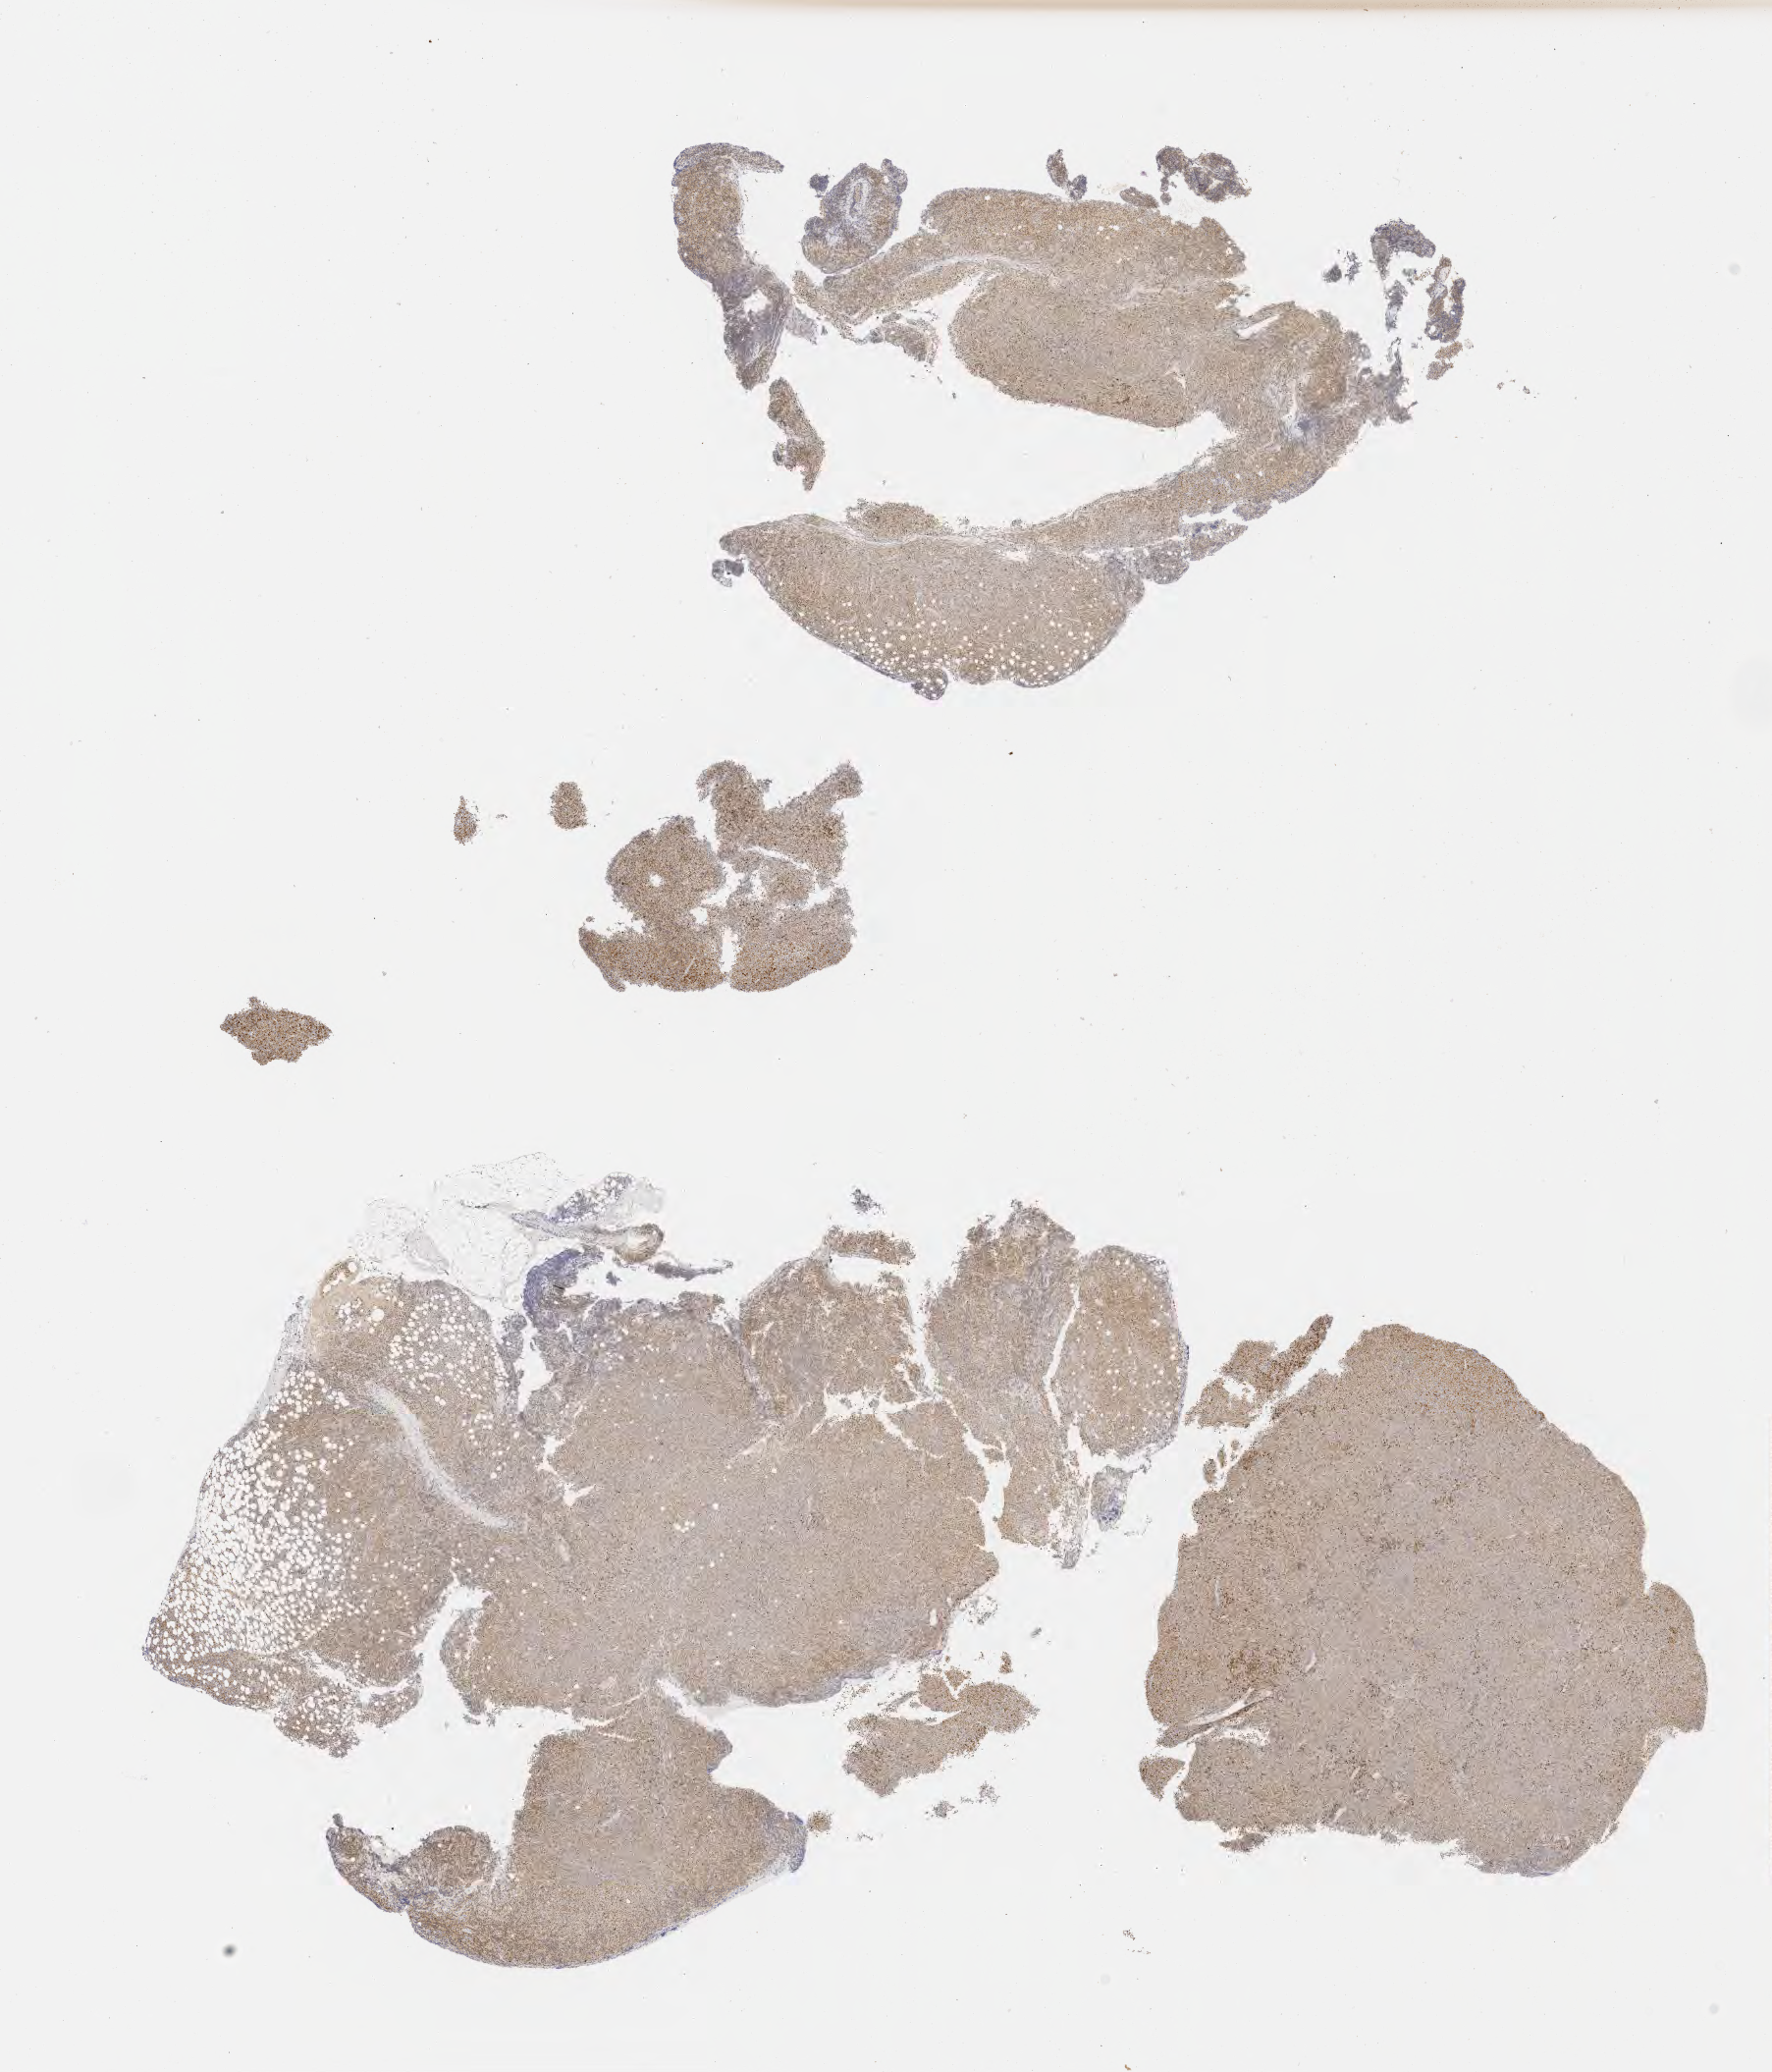
IHC for BCL6, whole-slide image — low-resolution overview of the scanned area, about 14.6 x 17.1 mm. Tumor tissue. Patient: female, age 32 years.
* histologic diagnosis: Diffuse large B-cell lymphoma, NOS